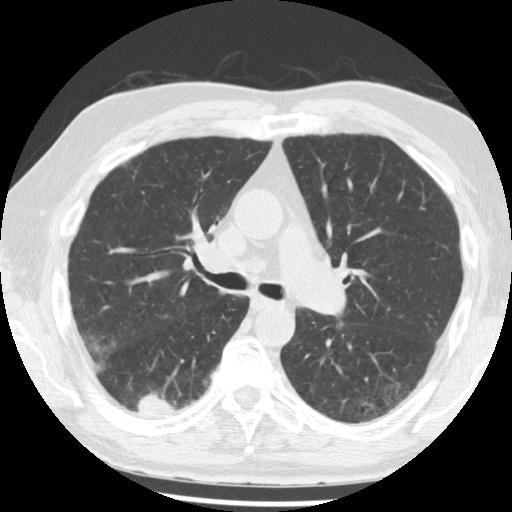
Low-dose screening chest CT, axial slice; third screening round (two years after baseline); lung window (W 1500 / L -600 HU); 2.5 mm slice thickness; standard (soft-tissue) reconstruction kernel (STANDARD). Male, age 68 years at enrolment. Current smoker at enrolment.
Expert-annotated lung lesion, bounding box (x1, y1, x2, y2) in pixels: (121, 378, 190, 429). The screening reader recorded 3 non-calcified nodules or masses ≥4 mm on this exam (right lower lobe, right lower lobe, right lower lobe); which of them this box marks is not recorded. Official screen result: positive, other. Lung cancer was diagnosed 48 days after this screen: squamous cell carcinoma, NOS, right lower lobe, moderately differentiated (G2), stage IB (AJCC 6th edition), 20 mm at pathology.